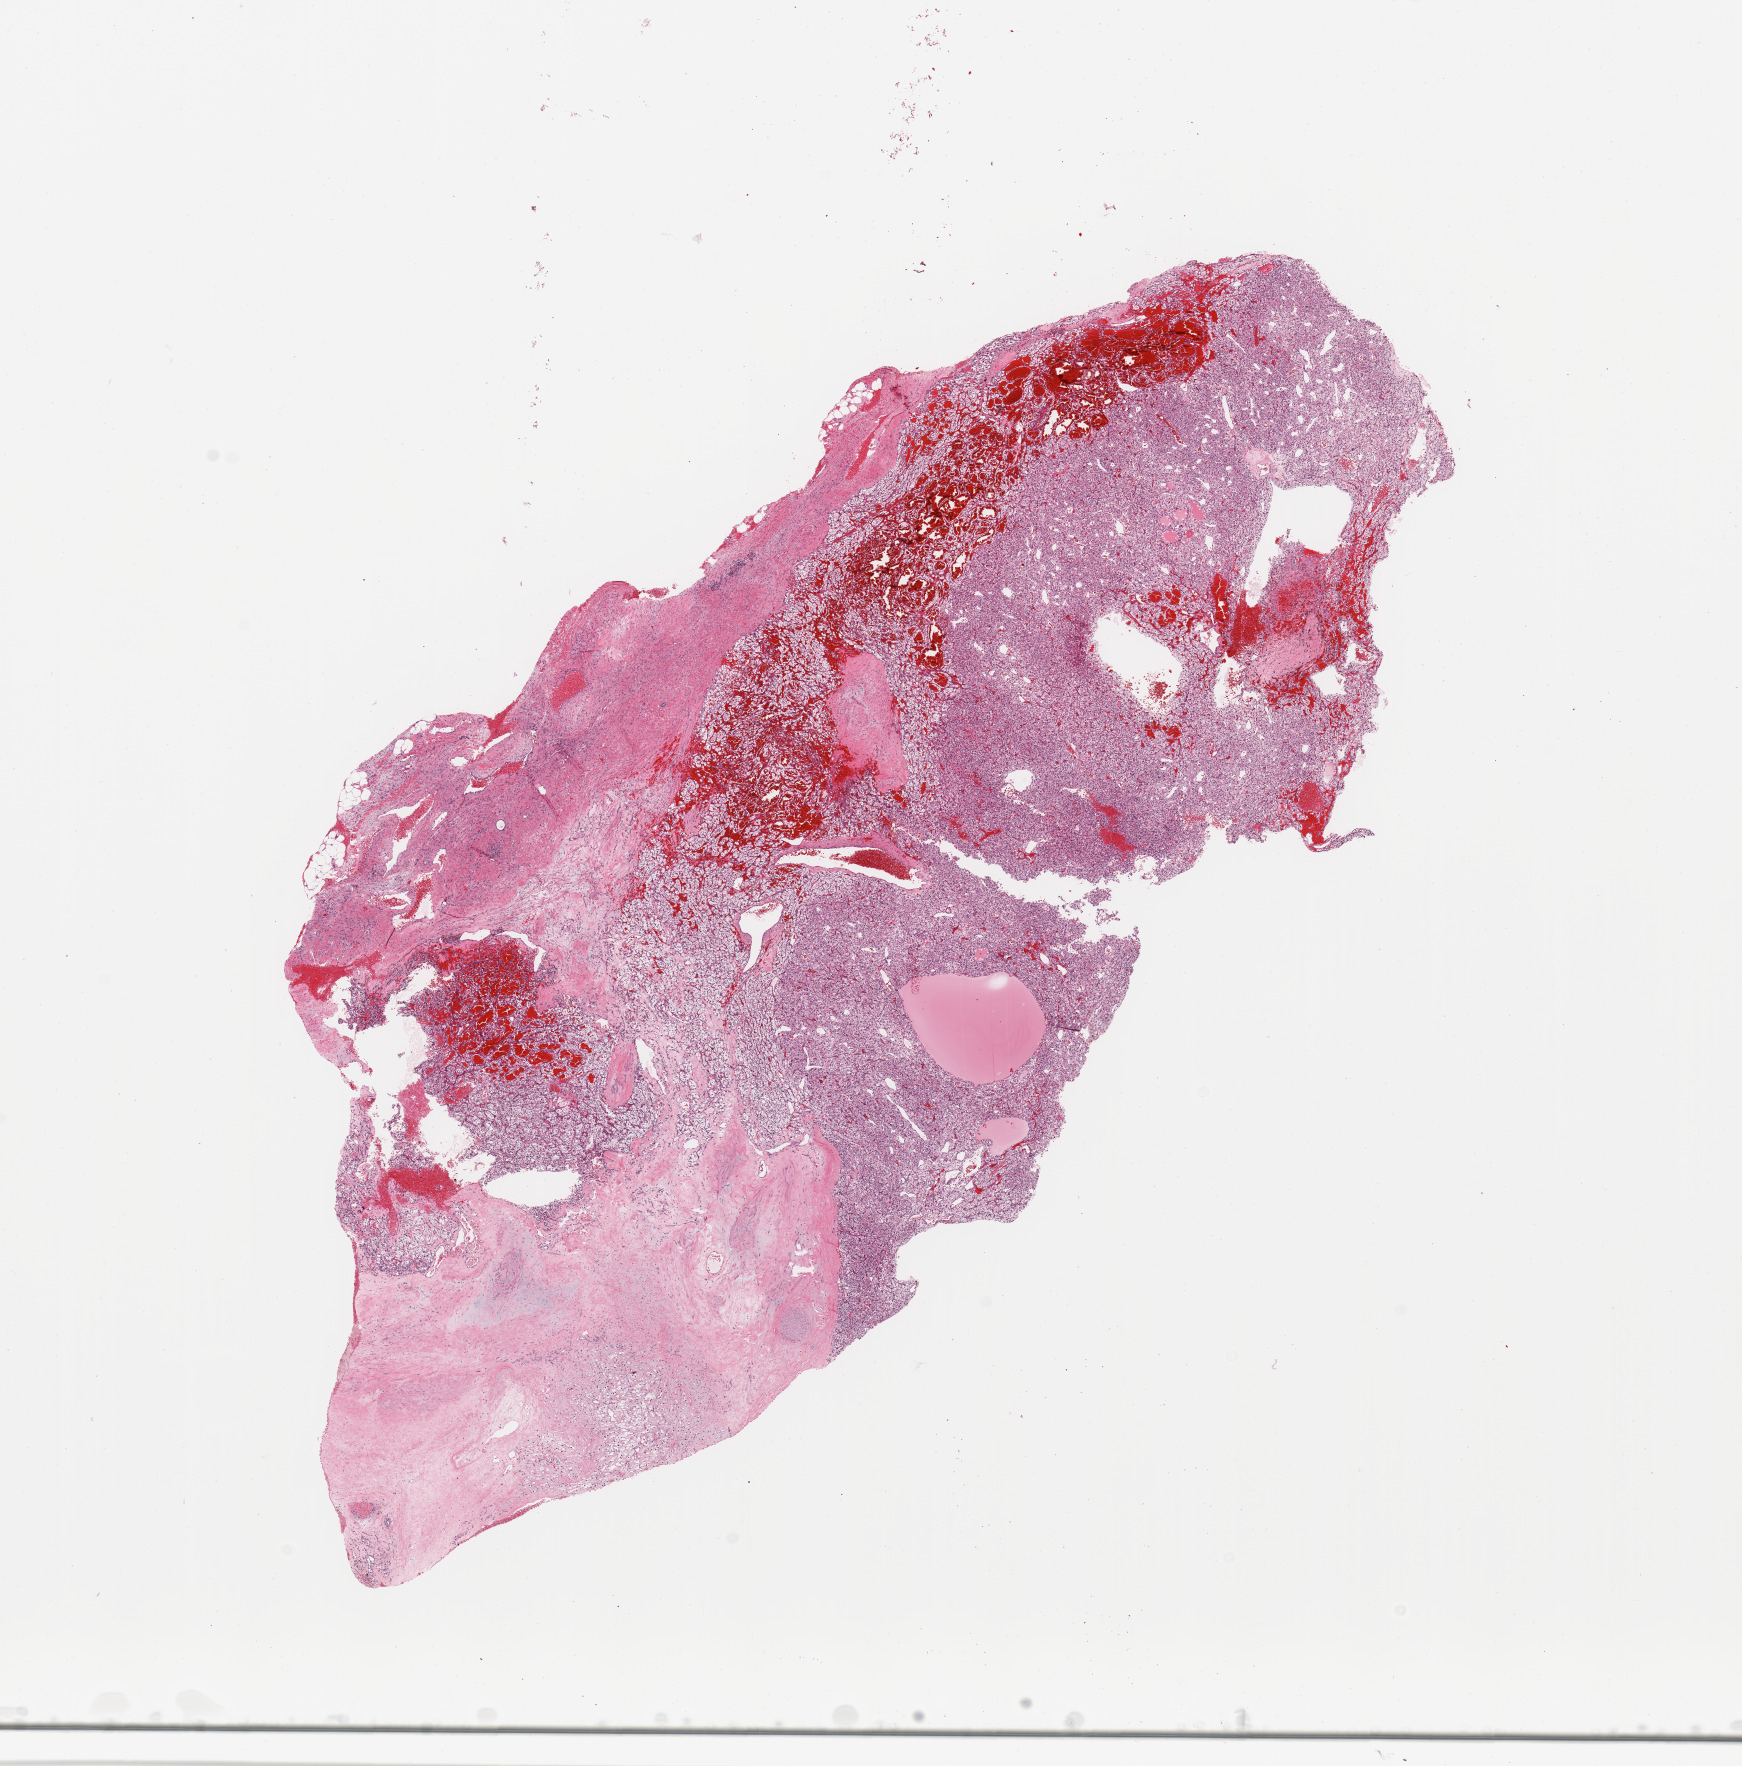
Whole-slide histology image, H&E-stained, a low-resolution overview of the entire scanned area, about 13.8 x 14.0 mm. Kidney, tumour tissue. Female, 75 y/o. Histologic grade: G3 (poorly differentiated).
AJCC pathologic stage: I. Primary tumour site (as recorded): upper pole. Histologic diagnosis: Renal cell carcinoma, NOS.